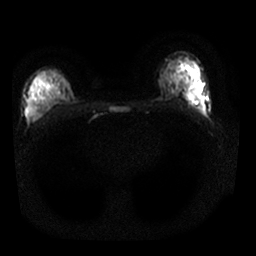
Breast MRI, one axial slice; slice 14 of 25 in the series (ordered by position); diffusion-weighted series; image 2 of 4 stored at this slice position (different b-values; order by instance number); 1.5 T; 4 mm slice thickness; 256 × 256 image matrix, field of view 320 × 320 mm. Female patient.
Annotated regions visible in this slice (expert manual segmentation):
- tumour on diffusion-weighted imaging: bounding box [x1, y1, x2, y2] px = [188, 95, 201, 102]